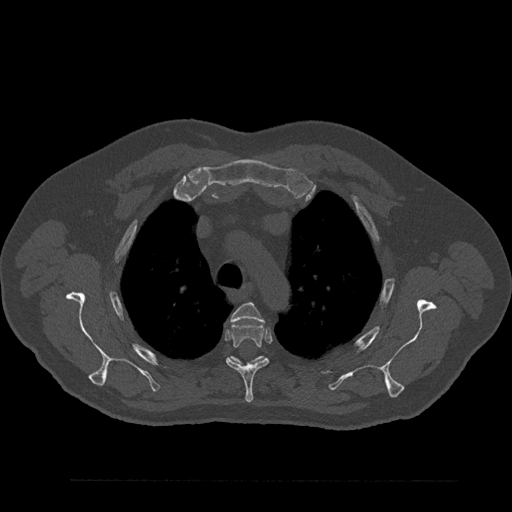
CT including the spine, one axial slice. Slice 643 of 797 in the series (ordered by position). Reconstruction kernel Br40s/3. Bone window (W 1800 / L 400 HU). 0.5 mm slice thickness. 512 × 512 image matrix. Male patient, age 61 years. From the clinical record (not read from this slice): primary cancer: prostate.
Outlined on this slice (semi-automatic segmentation, software-assisted and operator-edited):
- T3 vertebra: bounding box <231,303,264,322> (left, top, right, bottom; pixels)
- T4 vertebra: <226,323,269,403>
- T5 vertebra: <230,356,265,366>